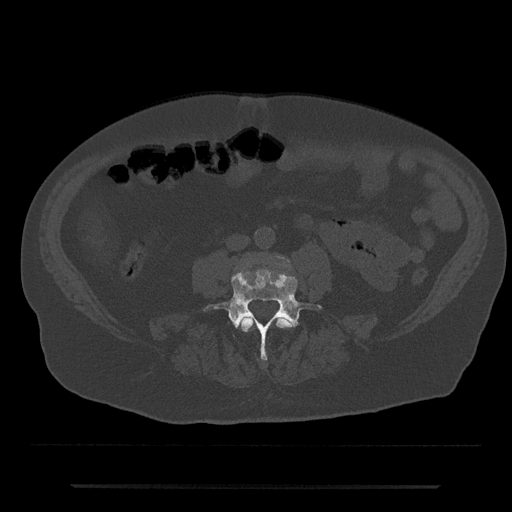
CT including the spine, one axial slice. Slice 364 of 797 in the series (ordered by position). Reconstruction kernel Br40s/3. 120 kVp. Bone window (W 1800 / L 400 HU). 0.5 mm slice thickness. 512 × 512 image matrix, field of view 434 × 434 mm. Male patient, age 80 years. From the clinical record (not read from this slice): primary cancer: prostate; vertebrae with lytic lesions (as recorded): L1, T11.
Annotated regions visible in this slice (semi-automatically segmented with operator editing):
- L3 vertebra: bounding box (x1, y1, x2, y2) in pixels: (239, 317, 293, 332)
- L4 vertebra: (204, 269, 322, 360)